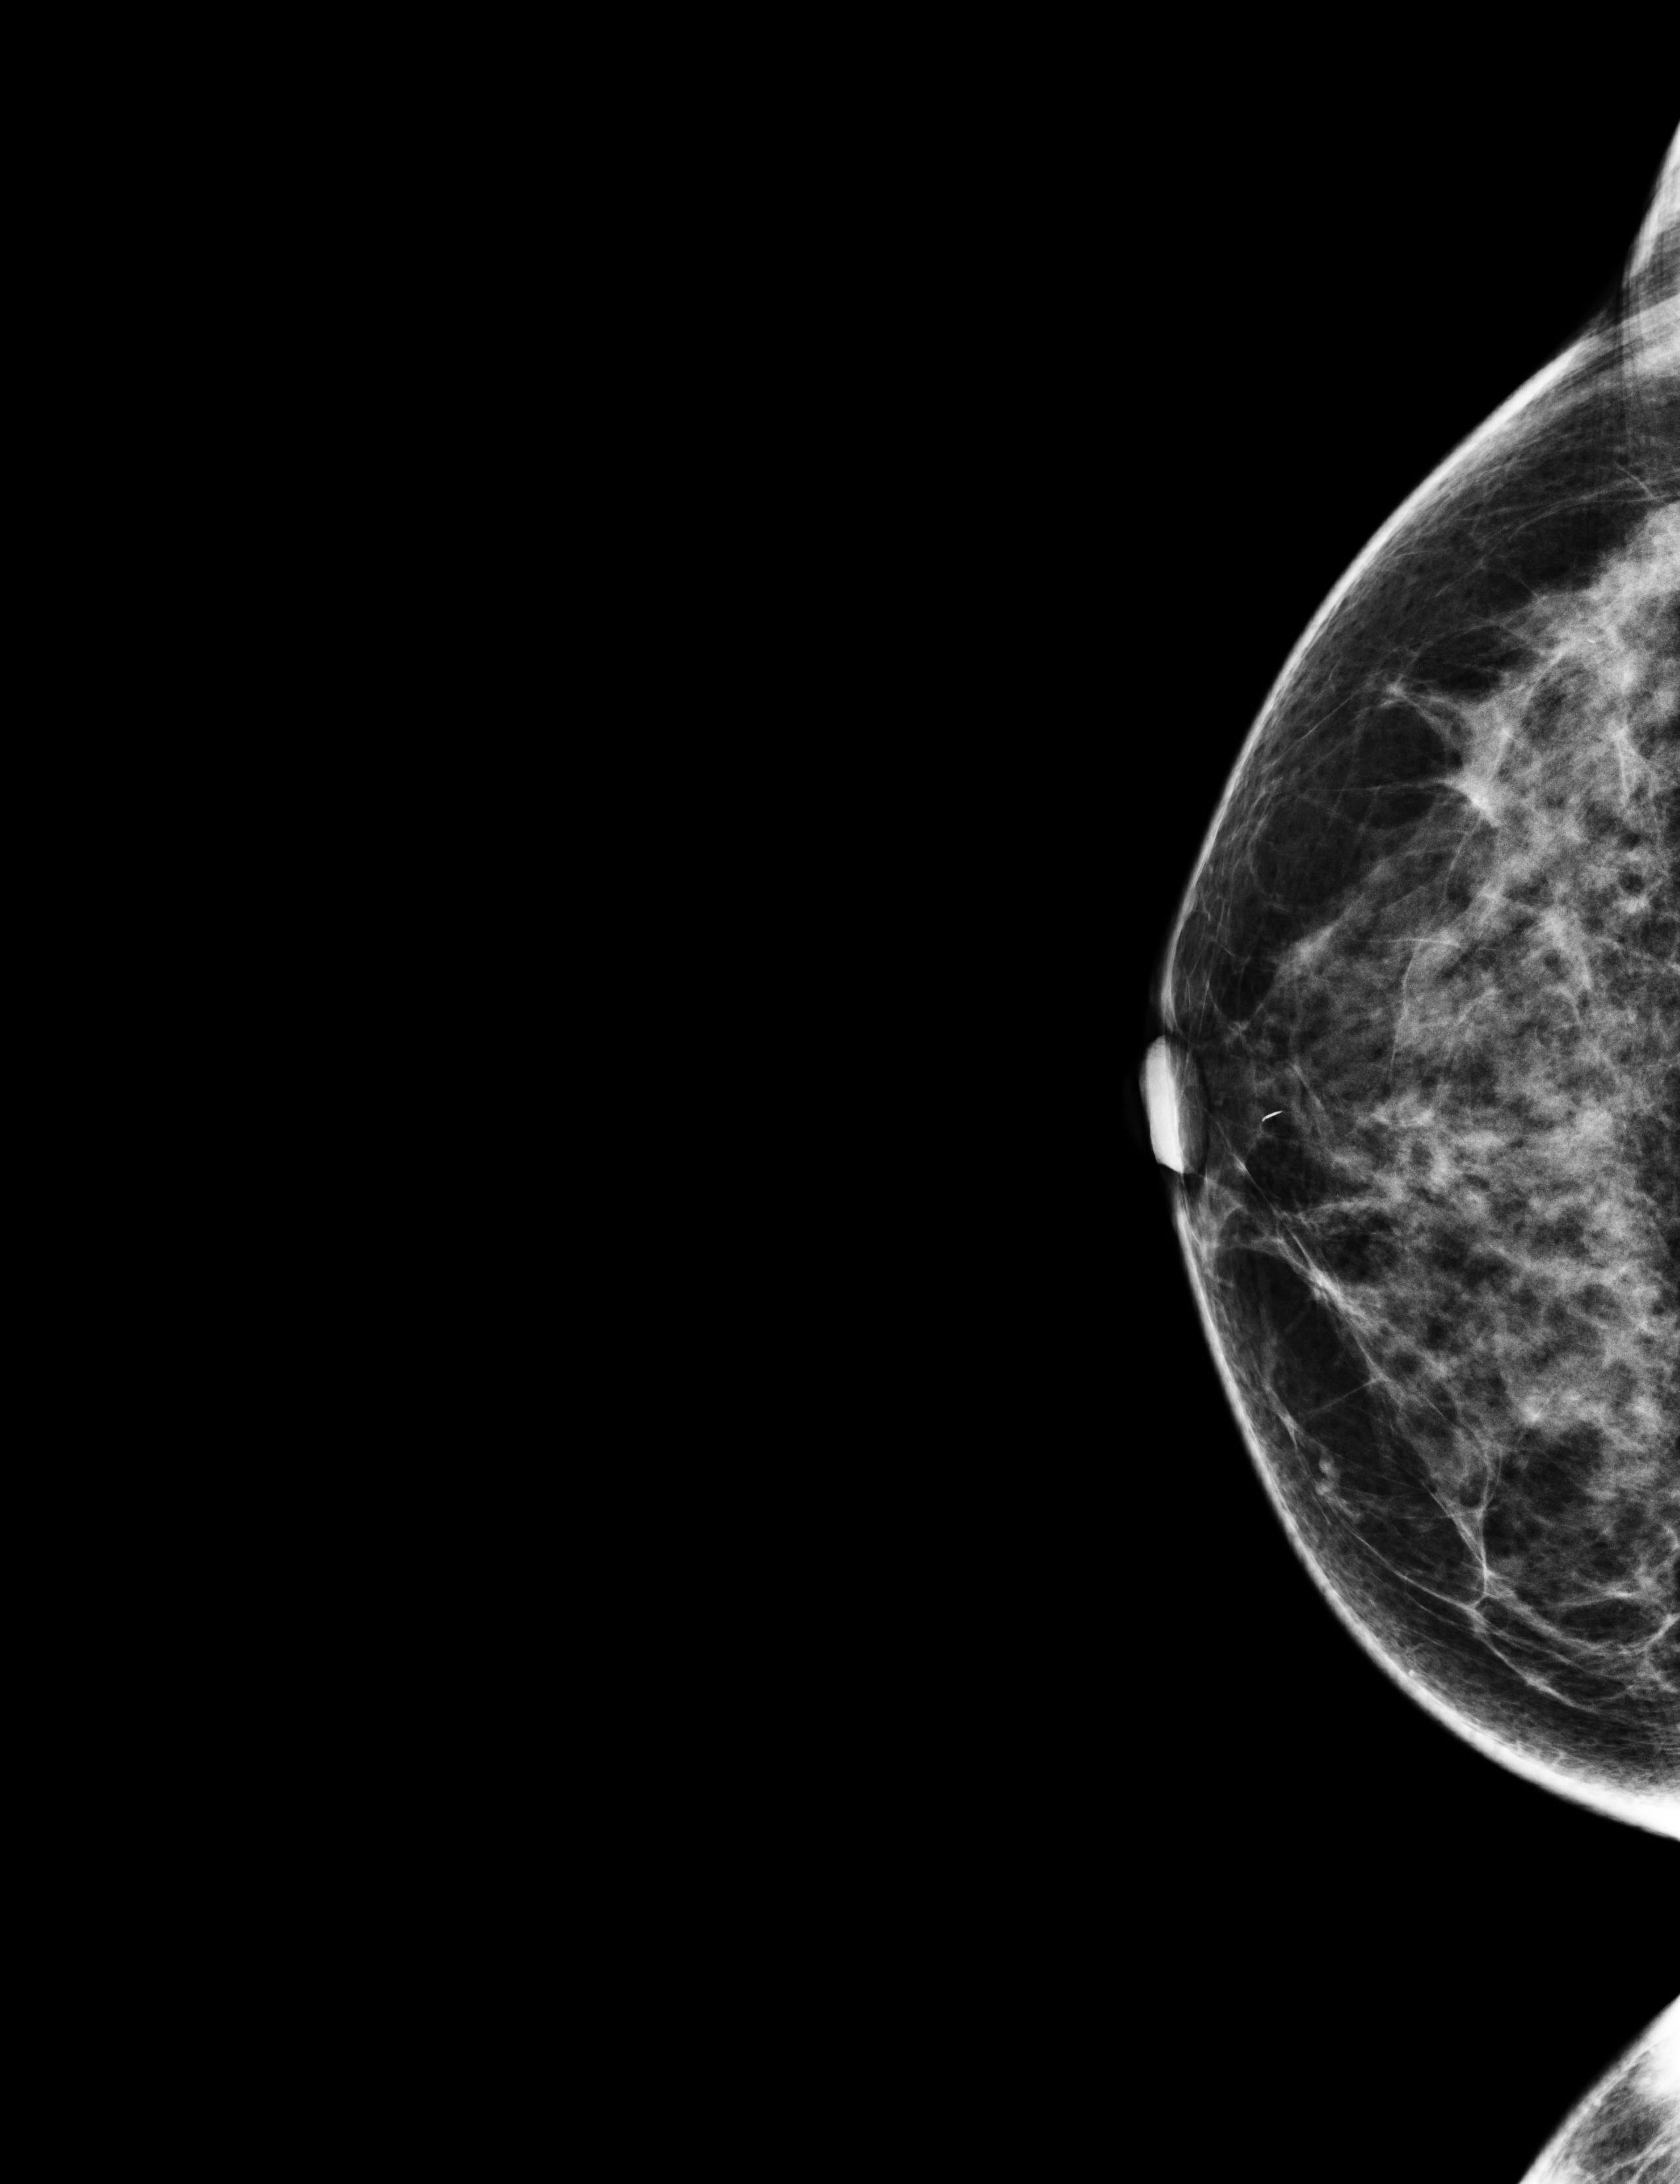
Screening examination. Female patient, age 55 years.
Image type: full-field digital mammogram. Breast: right. Projection: craniocaudal (CC) view.